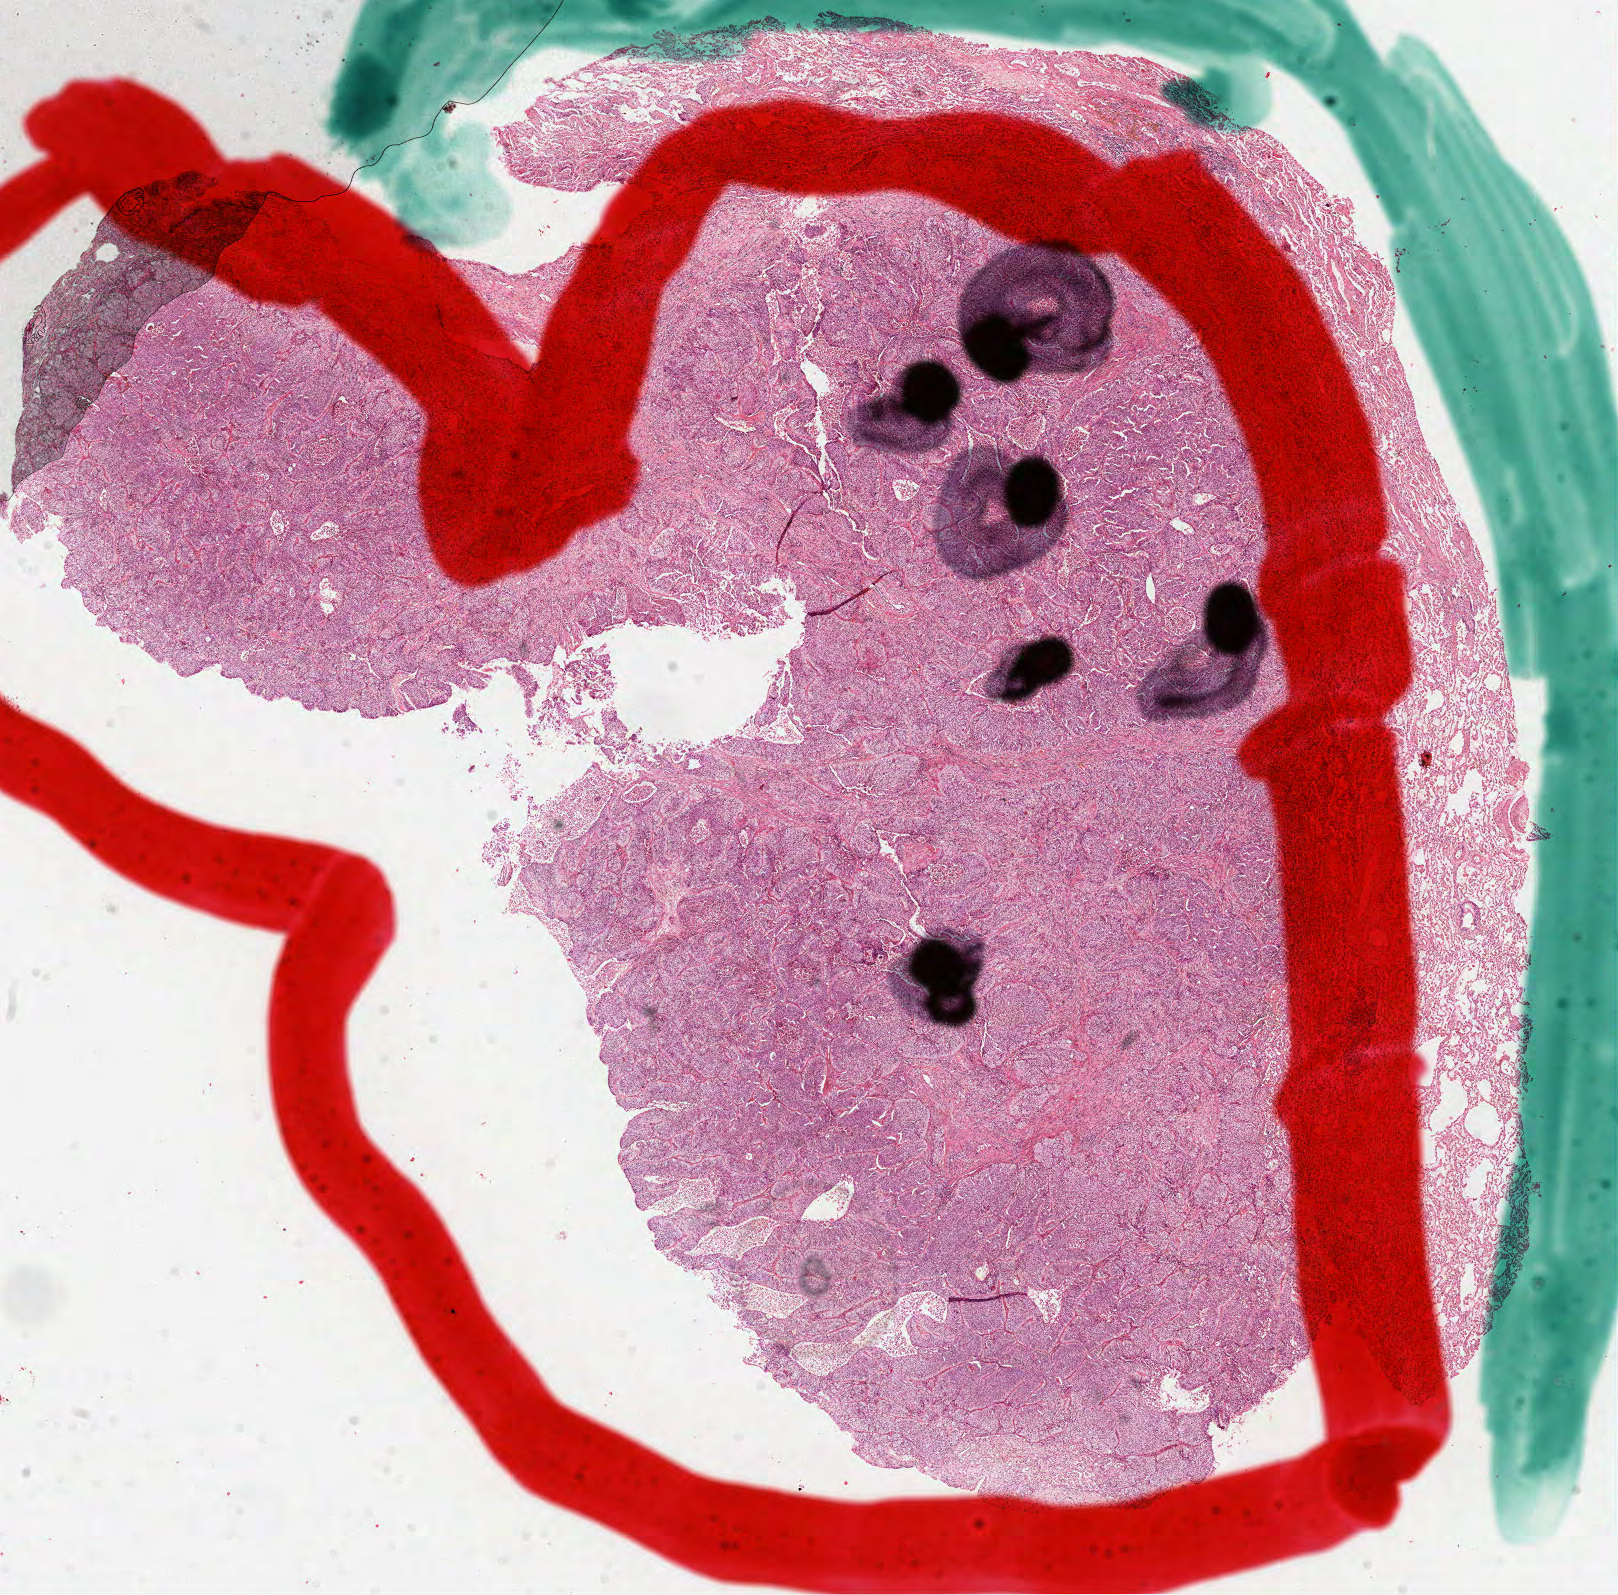
Digitized H&E-stained tissue section (whole slide), shown as a low-resolution overview of the whole scanned area (about 13.1 x 12.9 mm, acquisition: 40x scan). Formalin-fixed paraffin-embedded (FFPE) diagnostic section. Sample: primary tumour, lung. Female, age 59 years at initial diagnosis.
AJCC pathologic stage: IA (7th edition). Laterality: left. Histologic diagnosis: Squamous cell carcinoma, NOS (upper lobe, lung).